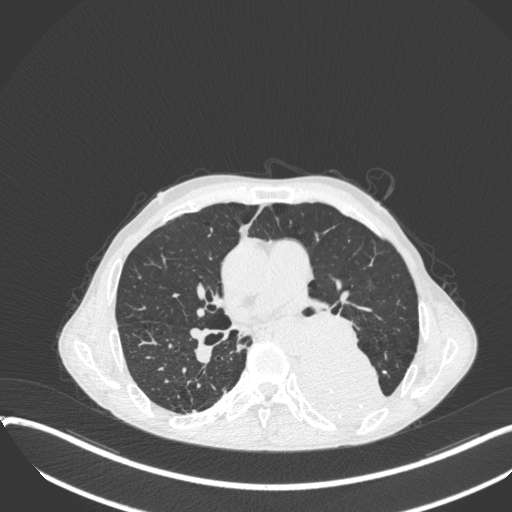
Chest CT, one axial slice; position 202 of 400 along the scan axis; reconstruction kernel B31f; 120 kVp; lung window (W 1500 / L -600 HU); 1 mm slice thickness; 512 × 512 image matrix. Patient: male, 57 years. From the clinical record (not read from this slice): clinical TNM (as recorded): T4 N0 M0.
Annotated regions visible in this slice (rectangle marked by the reading radiologist):
- lung tumour (recorded histology: squamous cell carcinoma): box from (x=296, y=343) to (x=392, y=428) px